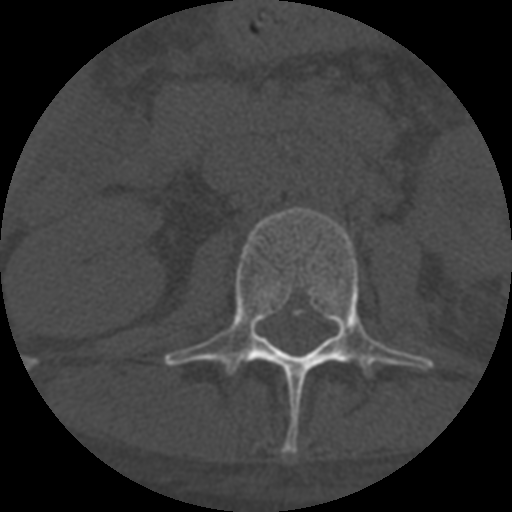
CT including the spine, one axial slice. Position 262 of 708 along the scan axis. Reconstruction kernel STANDARD. One of 3 acquisitions stored at this slice position. Bone window (W 1800 / L 400 HU). 512 × 512 image matrix, field of view 160 × 160 mm. Patient age 55 years. From the clinical record (not read from this slice): primary cancer: colon; vertebrae with lytic lesions (as recorded): T12, L1, L5.
Annotated regions visible in this slice (semi-automatic segmentation, software-assisted and operator-edited):
- L2 vertebra: bounding box [x1, y1, x2, y2] px = [164, 208, 434, 455]